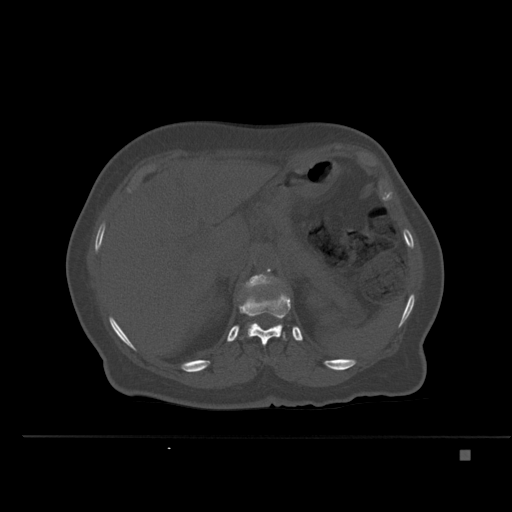
CT including the spine, one axial slice; position 251 of 477 along the scan axis; bone window (W 1800 / L 400 HU); 512 × 512 image matrix. Female patient, age 74 years. Case-level facts recorded for this patient, not image findings: primary cancer: colon.
Structures marked on this image (semi-automatically segmented with operator editing):
- L1 vertebra: bounding box <244,274,279,299> (left, top, right, bottom; pixels)
- T12 vertebra: <239,291,291,346>